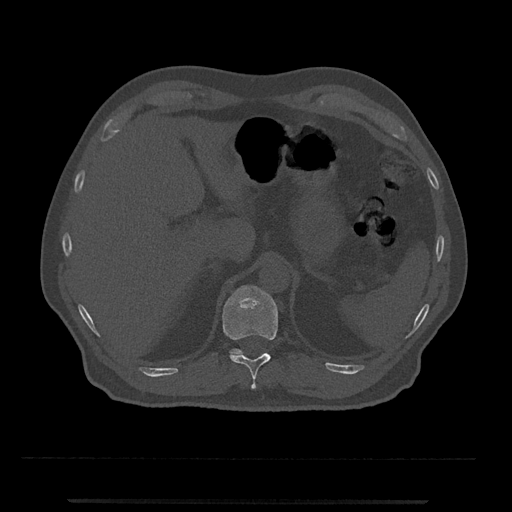
CT including the spine, one axial slice. Slice 452 of 797 in the series (ordered by position). Bone window (W 1800 / L 400 HU). 0.5 mm slice thickness. 512 × 512 image matrix, field of view 419 × 419 mm. Male patient, age 63 years. From the clinical record (not read from this slice): primary cancer: prostate.
Outlined on this slice (semi-automatically segmented with operator editing):
- T11 vertebra: bounding box [x1, y1, x2, y2] px = [222, 285, 278, 389]
- T12 vertebra: [230, 349, 244, 356]